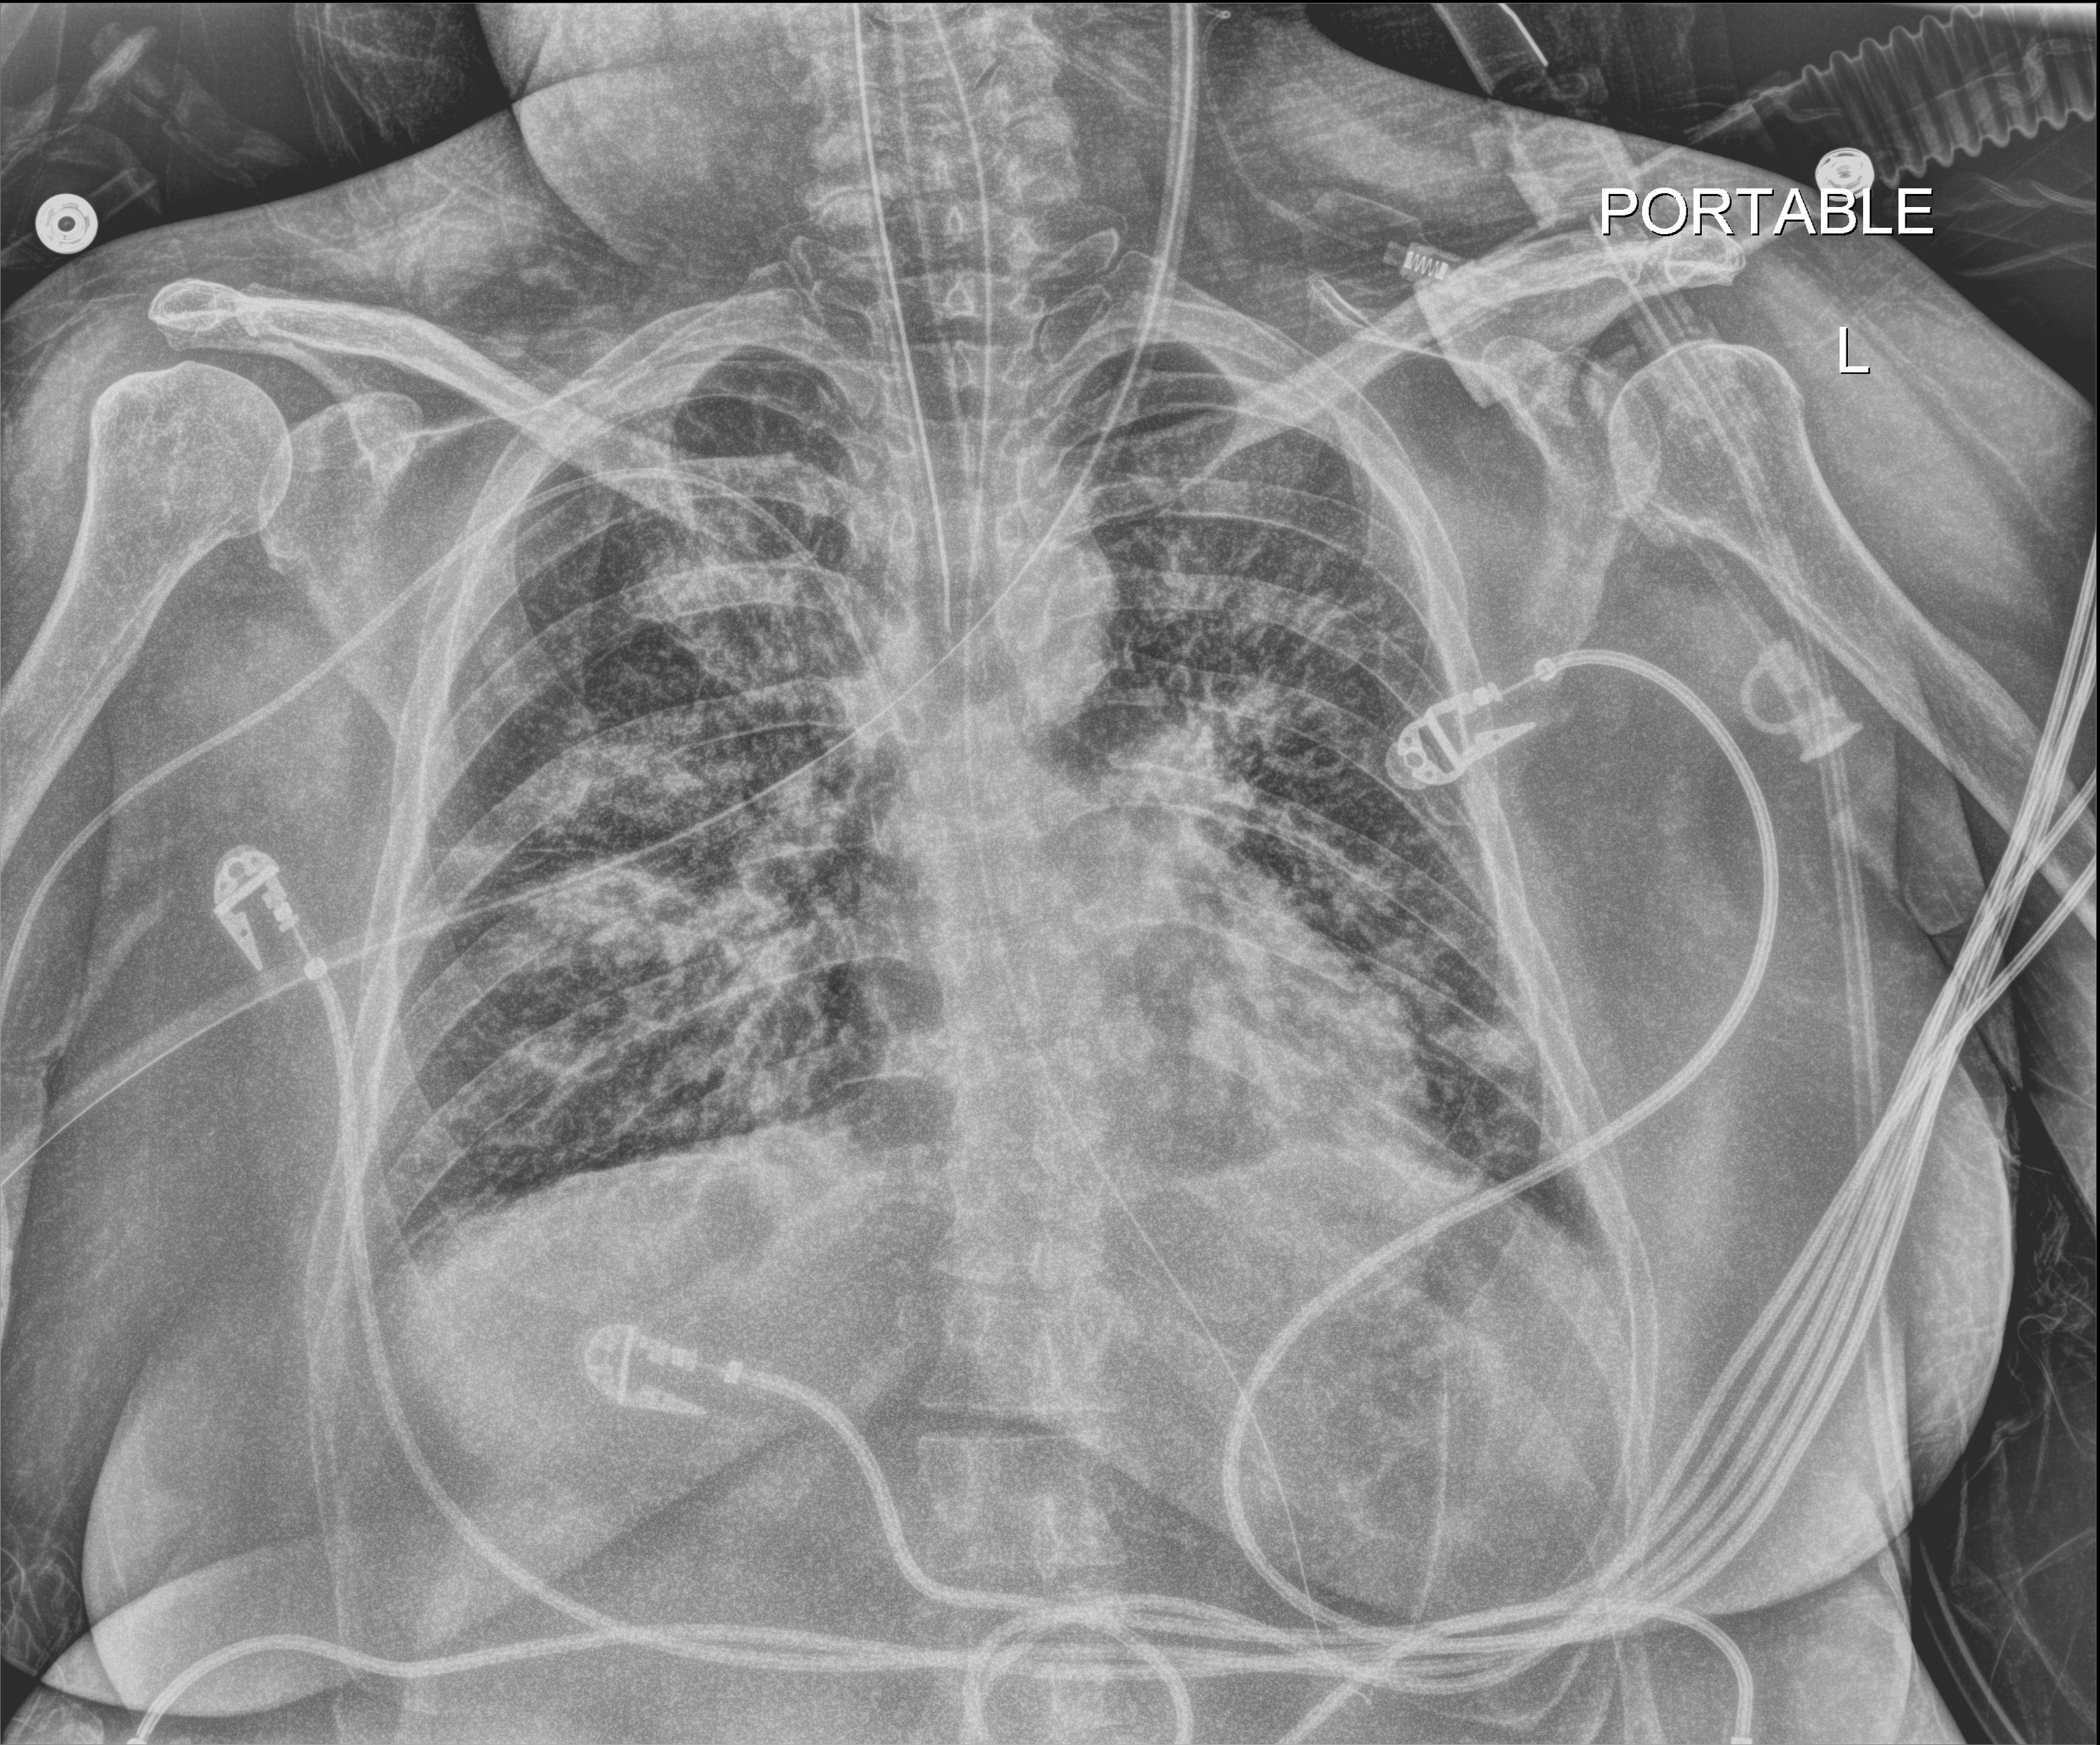
Chest radiograph; anteroposterior (AP) projection. Patient hospitalised with COVID-19, aged 18–59 years.
Admission-level facts for this patient (not findings on this image; timing relative to this image not recorded):
- mechanically ventilated during this hospital stay: yes